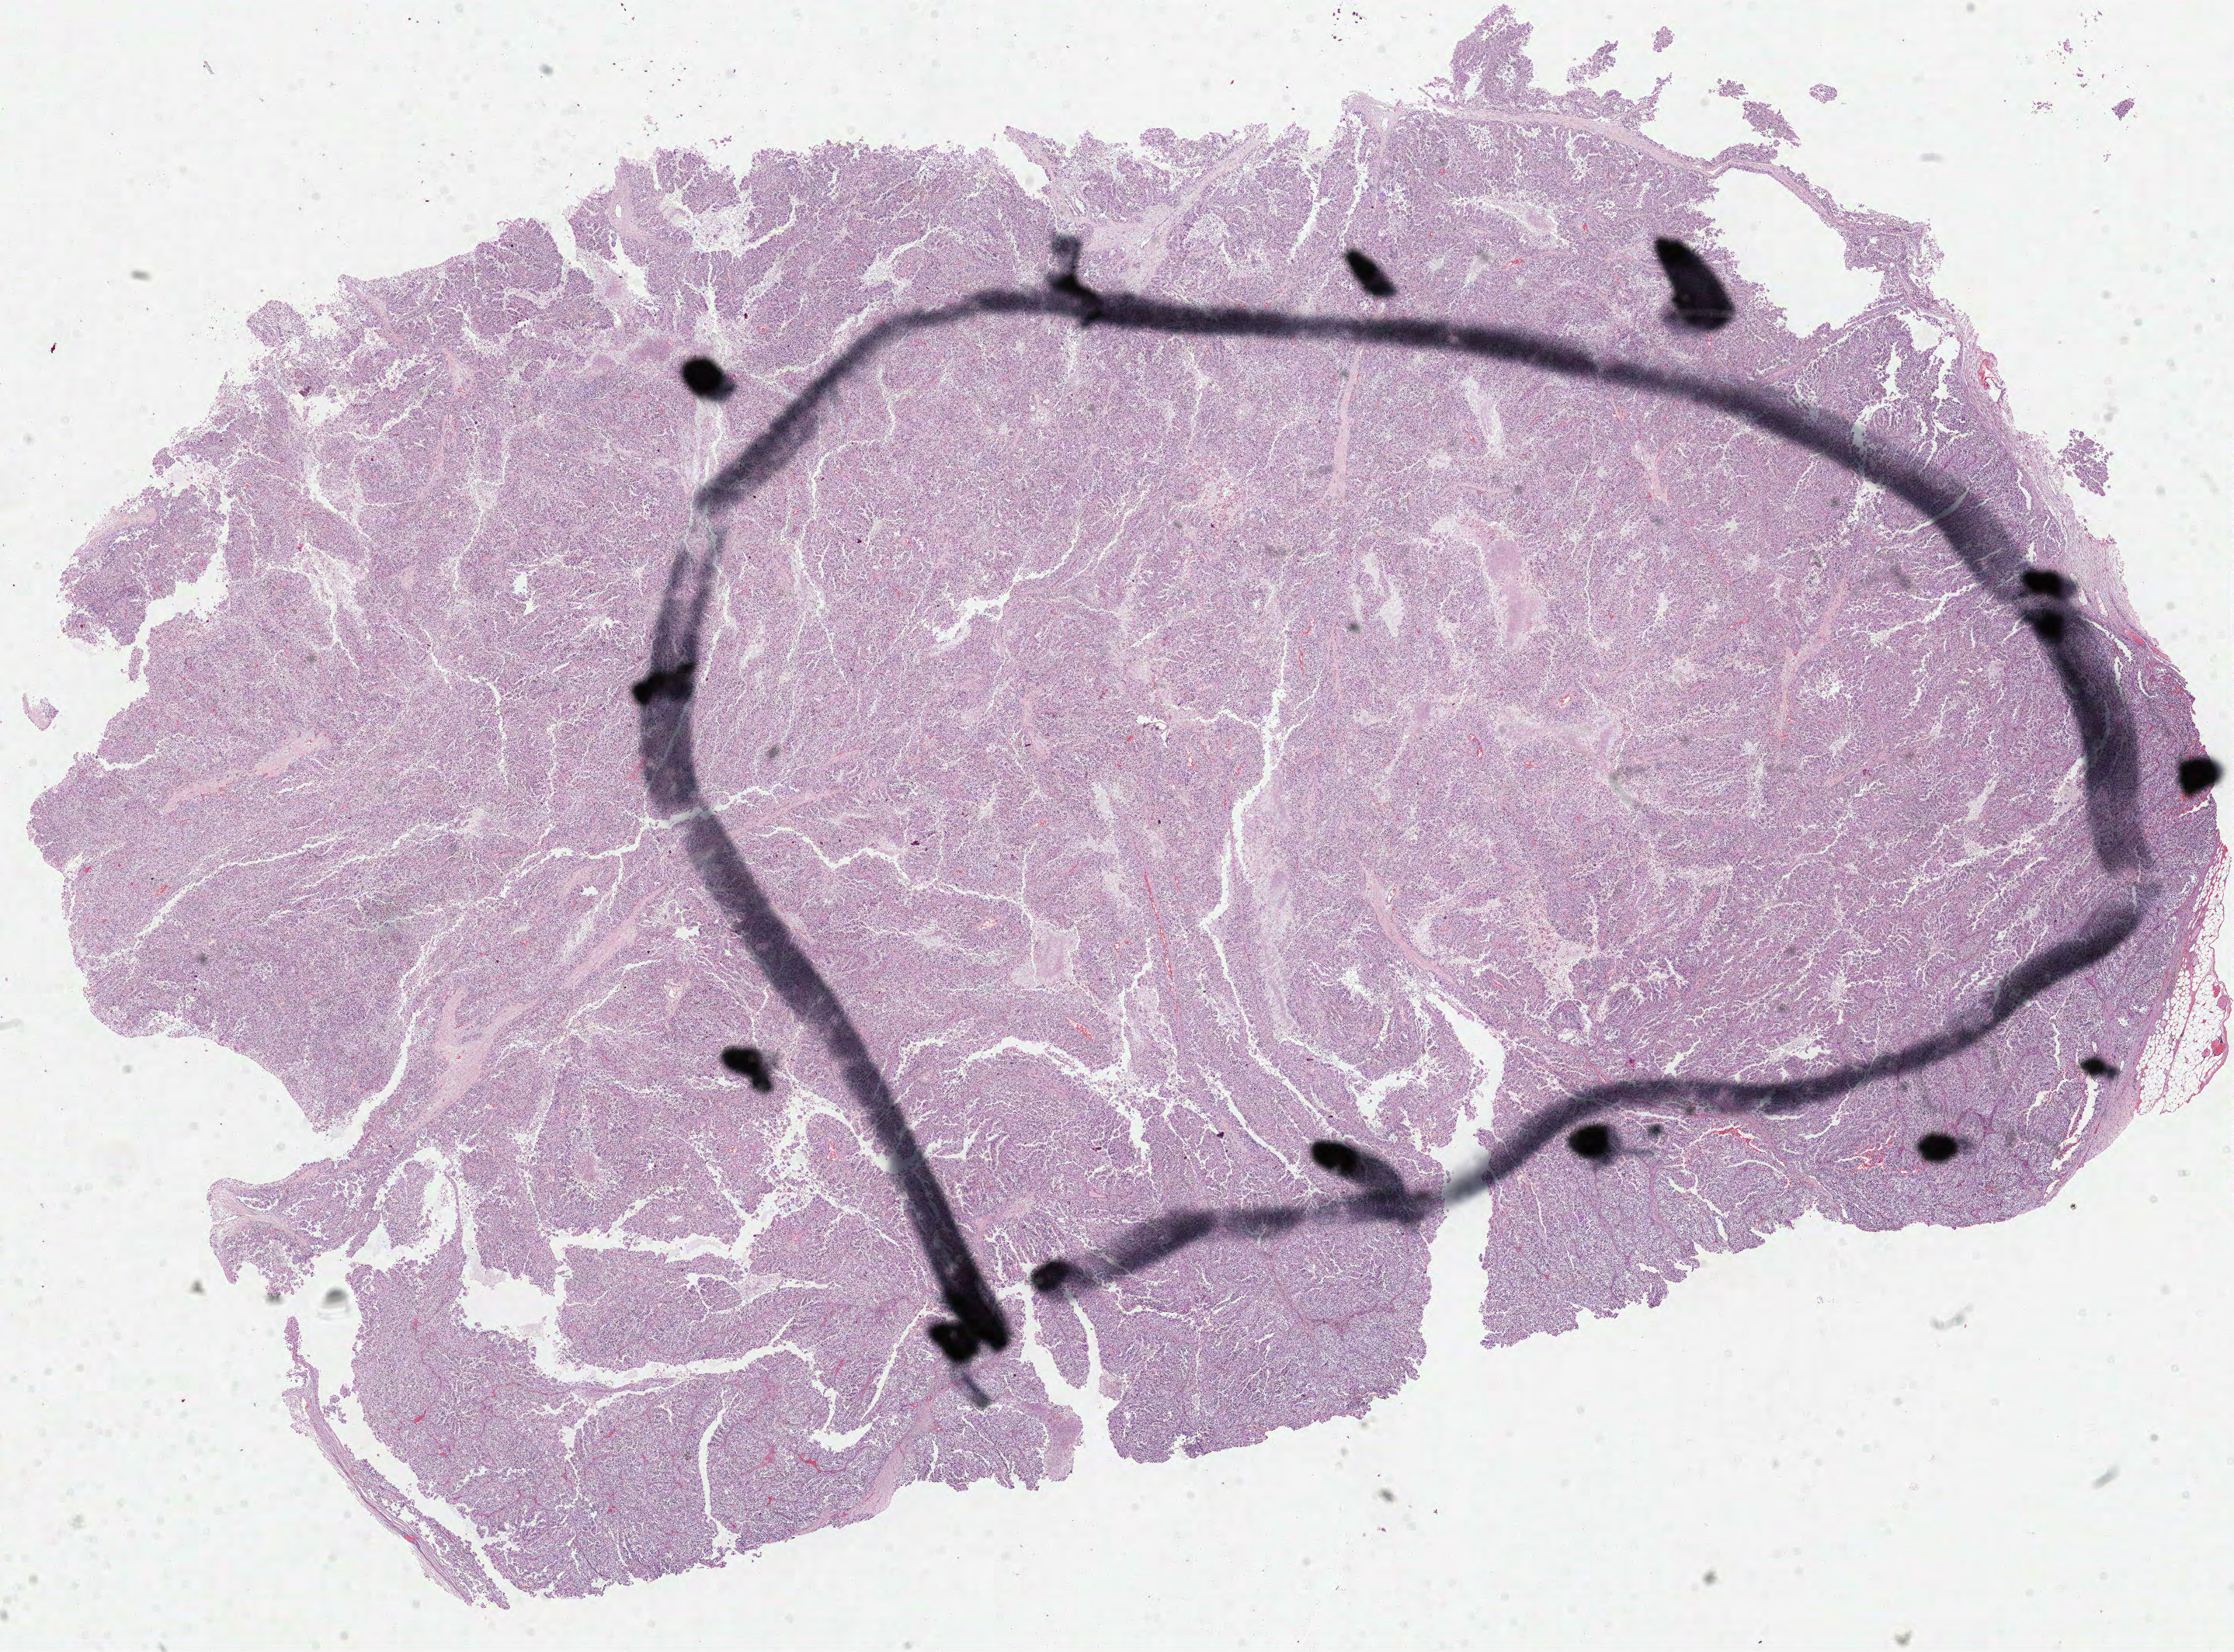
Whole-slide histology image, H&E-stained, a low-resolution overview of the entire scanned area, about 23.2 x 17.2 mm (from a 40x scan), formalin-fixed paraffin-embedded (FFPE) diagnostic section, kidney, primary tumour sample. Male patient; age at initial diagnosis 33 years. Histologic grade: G3 (poorly differentiated).
Diagnosis: Clear cell adenocarcinoma, NOS. AJCC pathologic stage: IV. Lymph nodes positive (case pathology): 1 of 1 examined. Laterality: right.